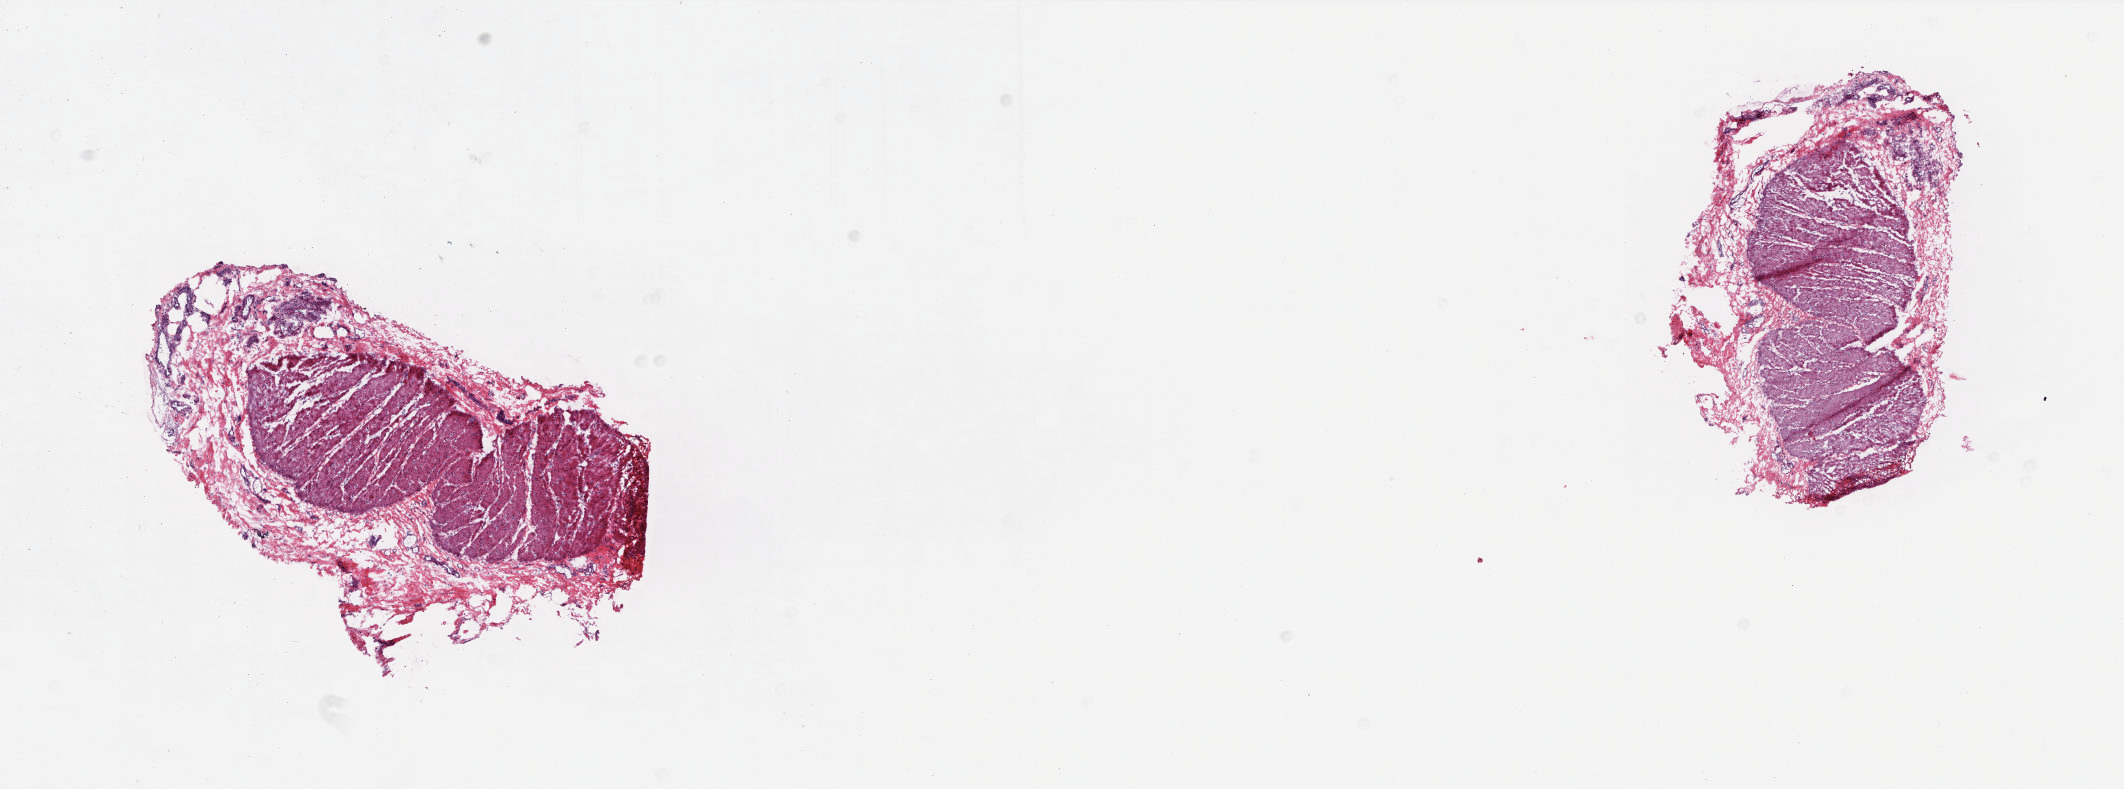
H&E-stained whole-slide image, a low-resolution overview of the entire scanned area, about 17.0 x 6.3 mm (from a 20x scan); frozen section from the top of the tissue portion; solid tissue normal (non-tumour tissue) sample from the rectum. Female, age 57 years at initial diagnosis. Composition of this section per pathologist review: tumour cells 0%, normal cells 100%. Infiltration values recorded for this section: lymphocyte infiltration 5%, monocyte infiltration 1%, neutrophil infiltration 0%.
This section: solid tissue normal (non-tumour) sample from the same patient. Patient diagnosis: Mucinous adenocarcinoma.